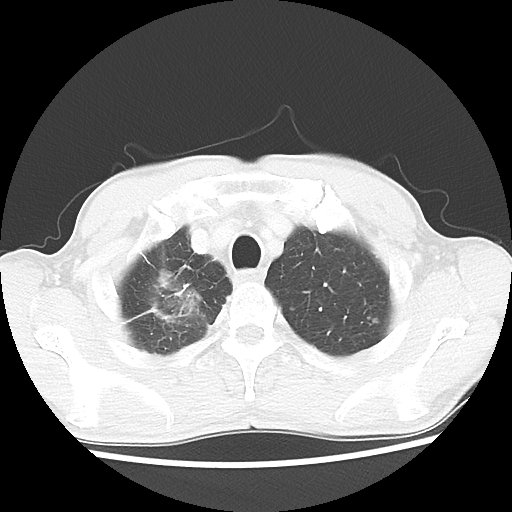
Chest CT, one axial slice. Reconstruction kernel LUNG. 100 kVp. Lung window (W 1500 / L -600 HU). 512 × 512 image matrix, field of view 323 × 323 mm. Male patient, age 66 years. Case-level facts recorded for this patient, not image findings: clinical TNM (as recorded): T2 N0 M1a.
Outlined on this slice (rectangle marked by the reading radiologist):
- lung tumour (recorded histology: adenocarcinoma): box from (x=149, y=264) to (x=206, y=331) px